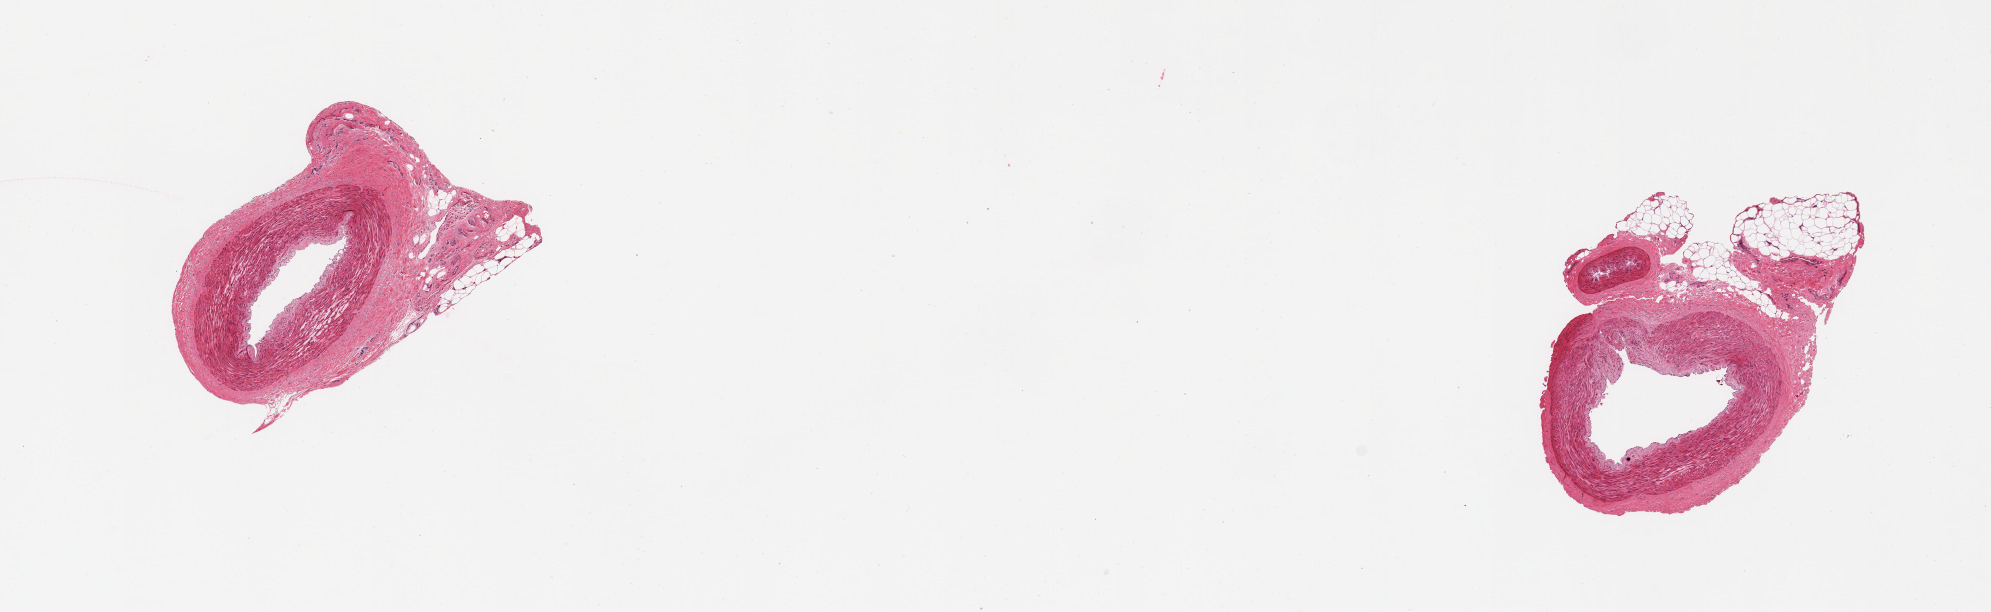
Whole-slide image, haematoxylin and eosin stain, brightfield — shown as a low-resolution overview of the whole scanned area (about 15.8 x 4.8 mm, slide scanned at 20x); PAXgene-fixed paraffin-embedded (PFPE) section; sampled site (target tissue): tibial nerve; donor tissue sample. Male donor.
Pathologist's review note for this sample: 1 piece; artery not nerve.